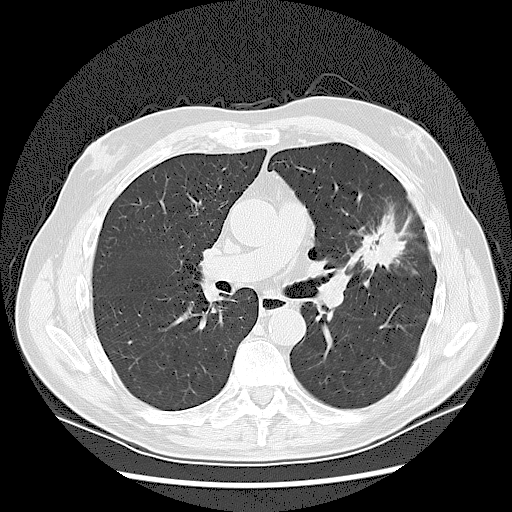
Low-dose screening chest CT, one axial slice. Reconstruction kernel LUNG. Lung window (W 1500 / L -600 HU). 2.5 mm slice thickness. 512 × 512 image matrix, field of view 380 × 380 mm.
Outlined on this slice (expert manual segmentation):
- lesion 1 (tumor, upper lobe of left lung): bounding box <360,227,405,263> (left, top, right, bottom; pixels)